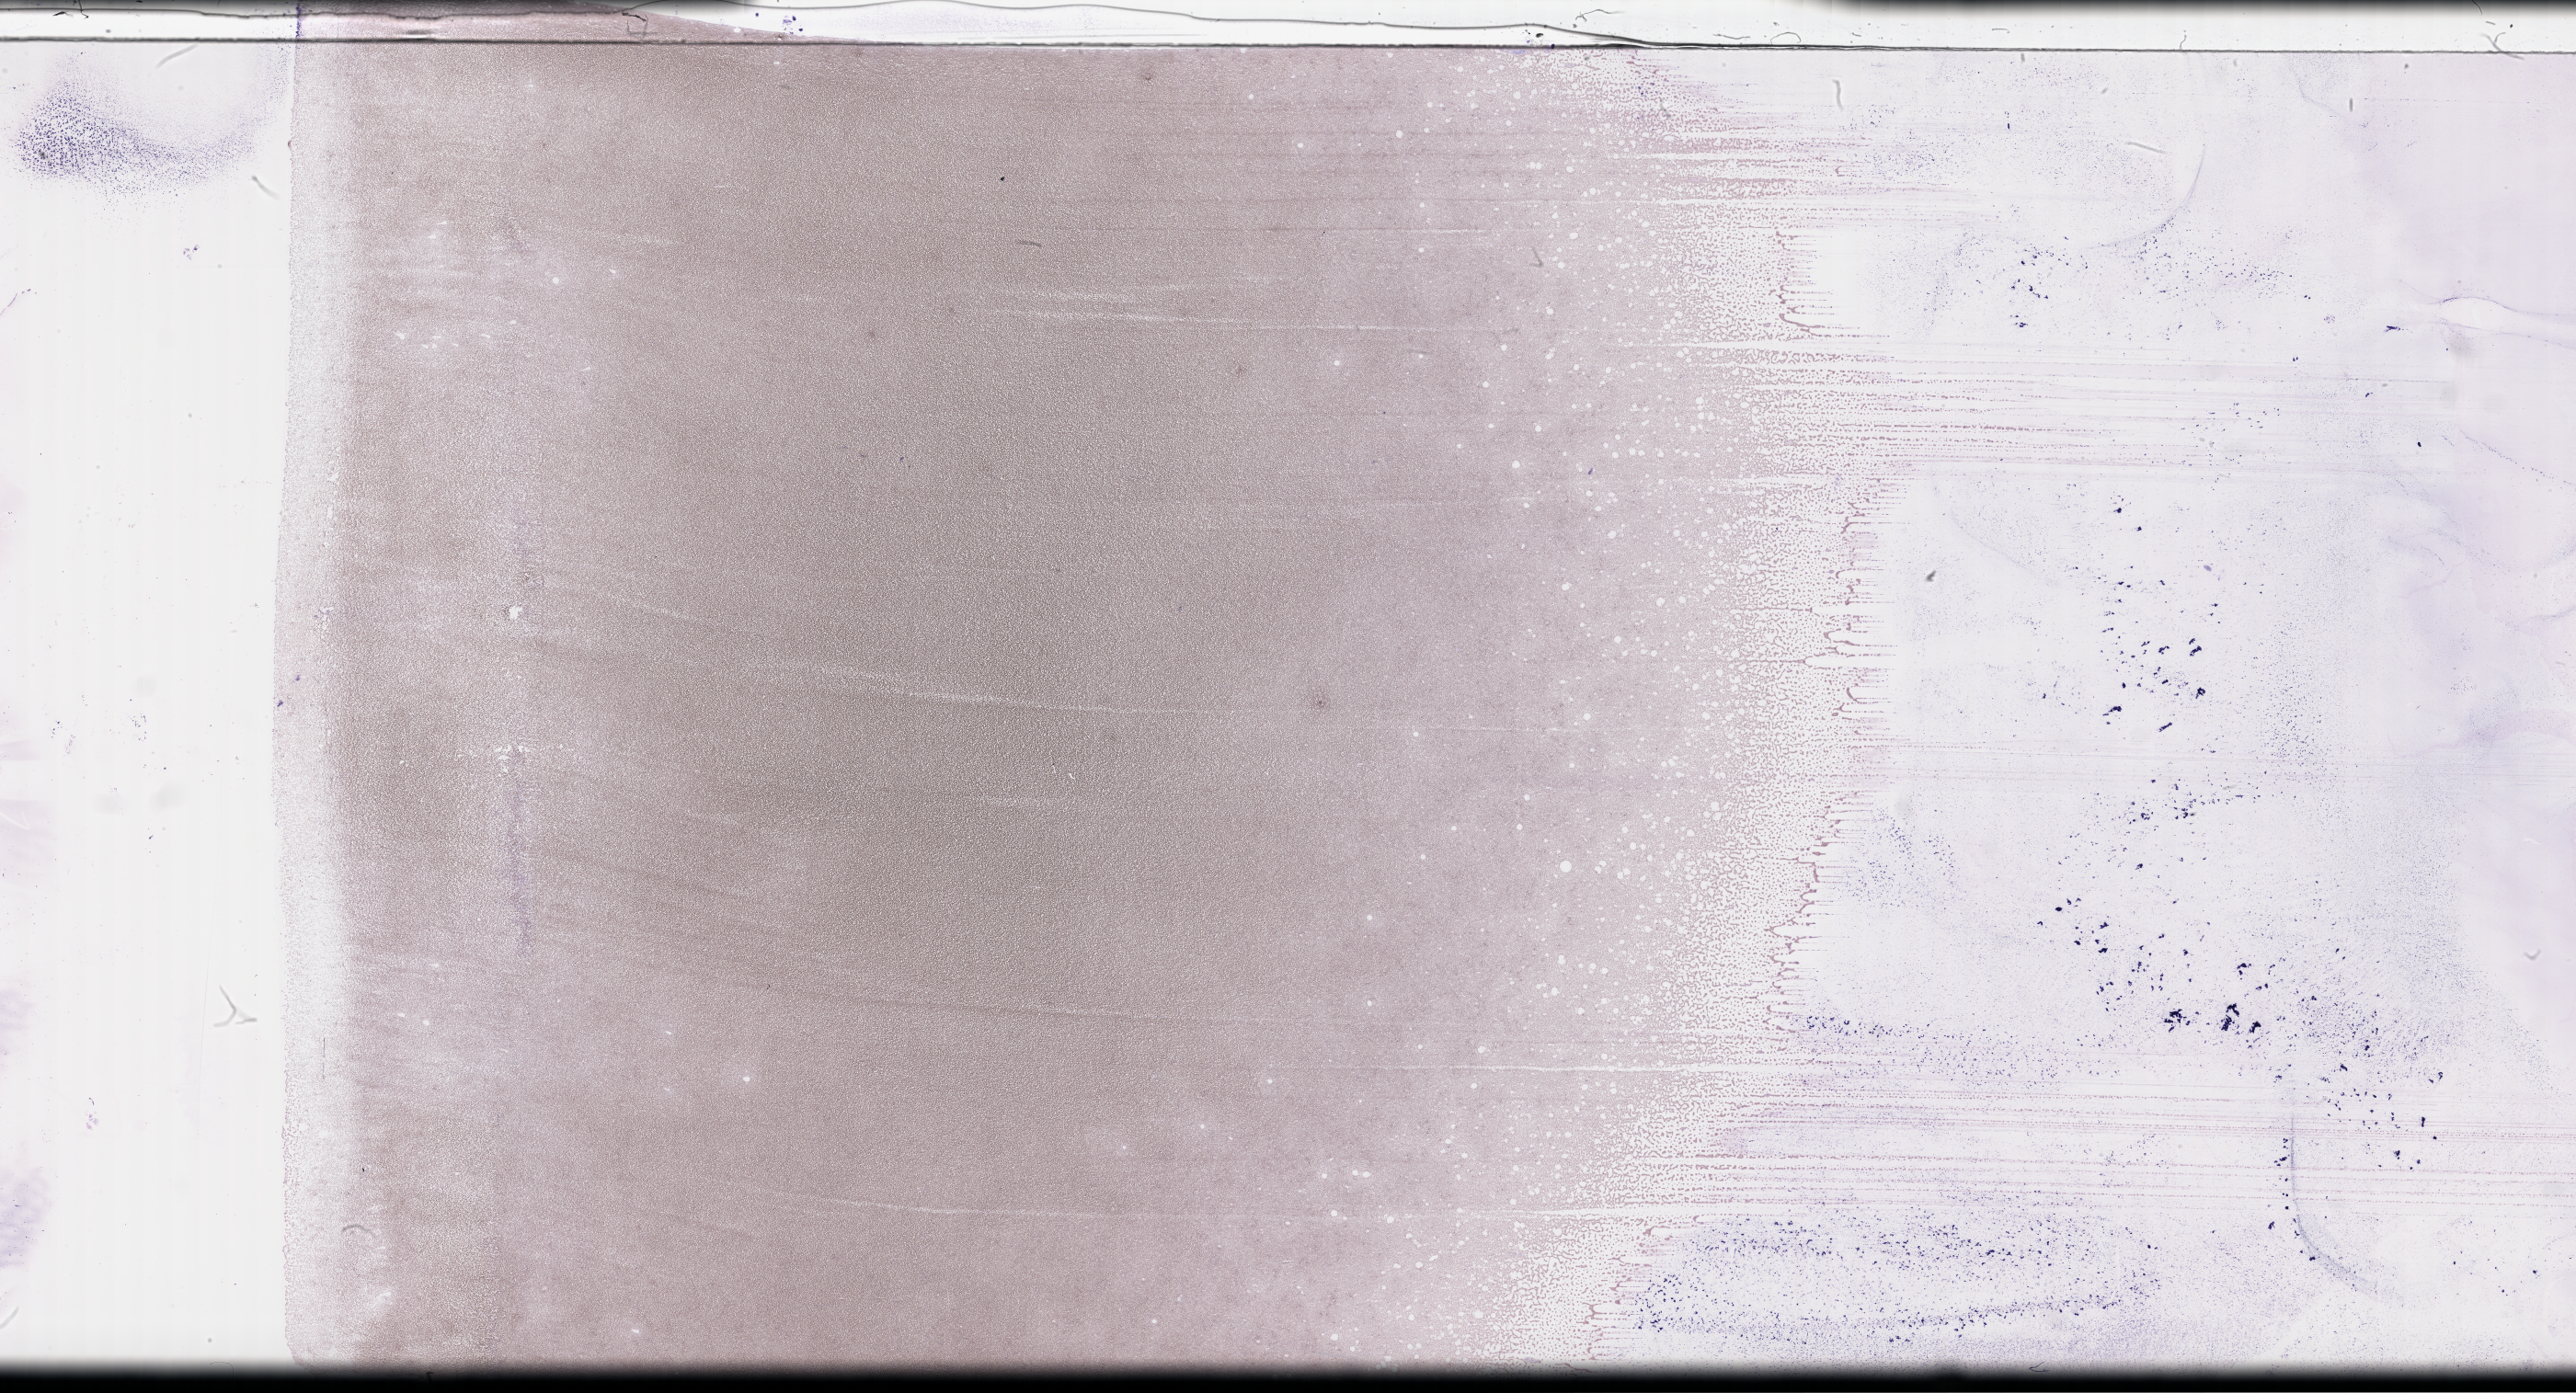
Wright–Giemsa-stained whole blood smear, whole-slide image, low-resolution overview of the scanned area, about 45.2 x 24.5 mm. Collected on treatment. Patient sex: male.
From a patient with: Plasma Cell Myeloma.